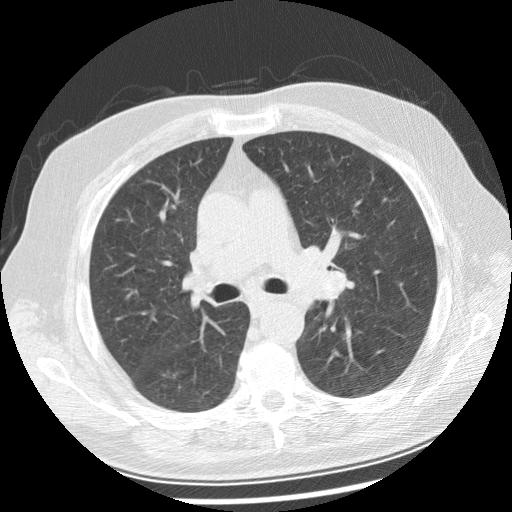
Low-dose screening chest CT, one axial slice; position 153 of 250 along the scan axis; 120 kVp; lung window (W 1500 / L -600 HU); 512 × 512 image matrix, field of view 360 × 360 mm.
Annotated regions visible in this slice (expert manual segmentation):
- lesion 1 (tumor, left main bronchus): bounding box (x1, y1, x2, y2) in pixels: (311, 271, 355, 301)